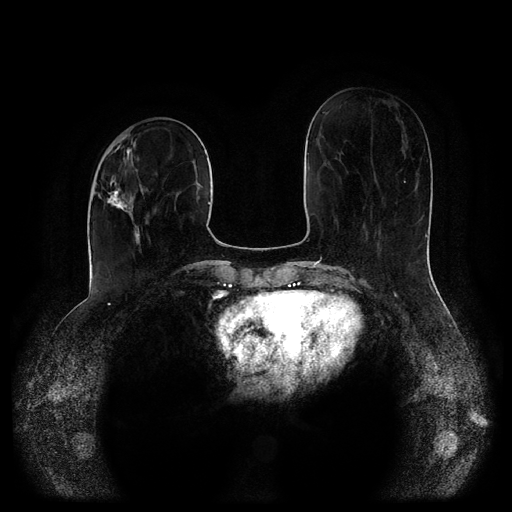
Breast MRI (dynamic contrast-enhanced, multi-phase), one axial slice; position 36 of 116 along the scan axis; dynamic contrast-enhanced series, time point 2 of 5 at this slice position (early post-contrast); 1.5 T; TE 2.6 ms, TR 5.2 ms; 2 mm slice thickness; 512 × 512 image matrix. Patient: female, 52 years.
Structures marked on this image (semi-automatically segmented with operator editing):
- breast lesion (labelled 'tumour' in the annotation; benign lesions carry a separate 'benign' label): bounding box (x1, y1, x2, y2) in pixels: (98, 175, 141, 244)